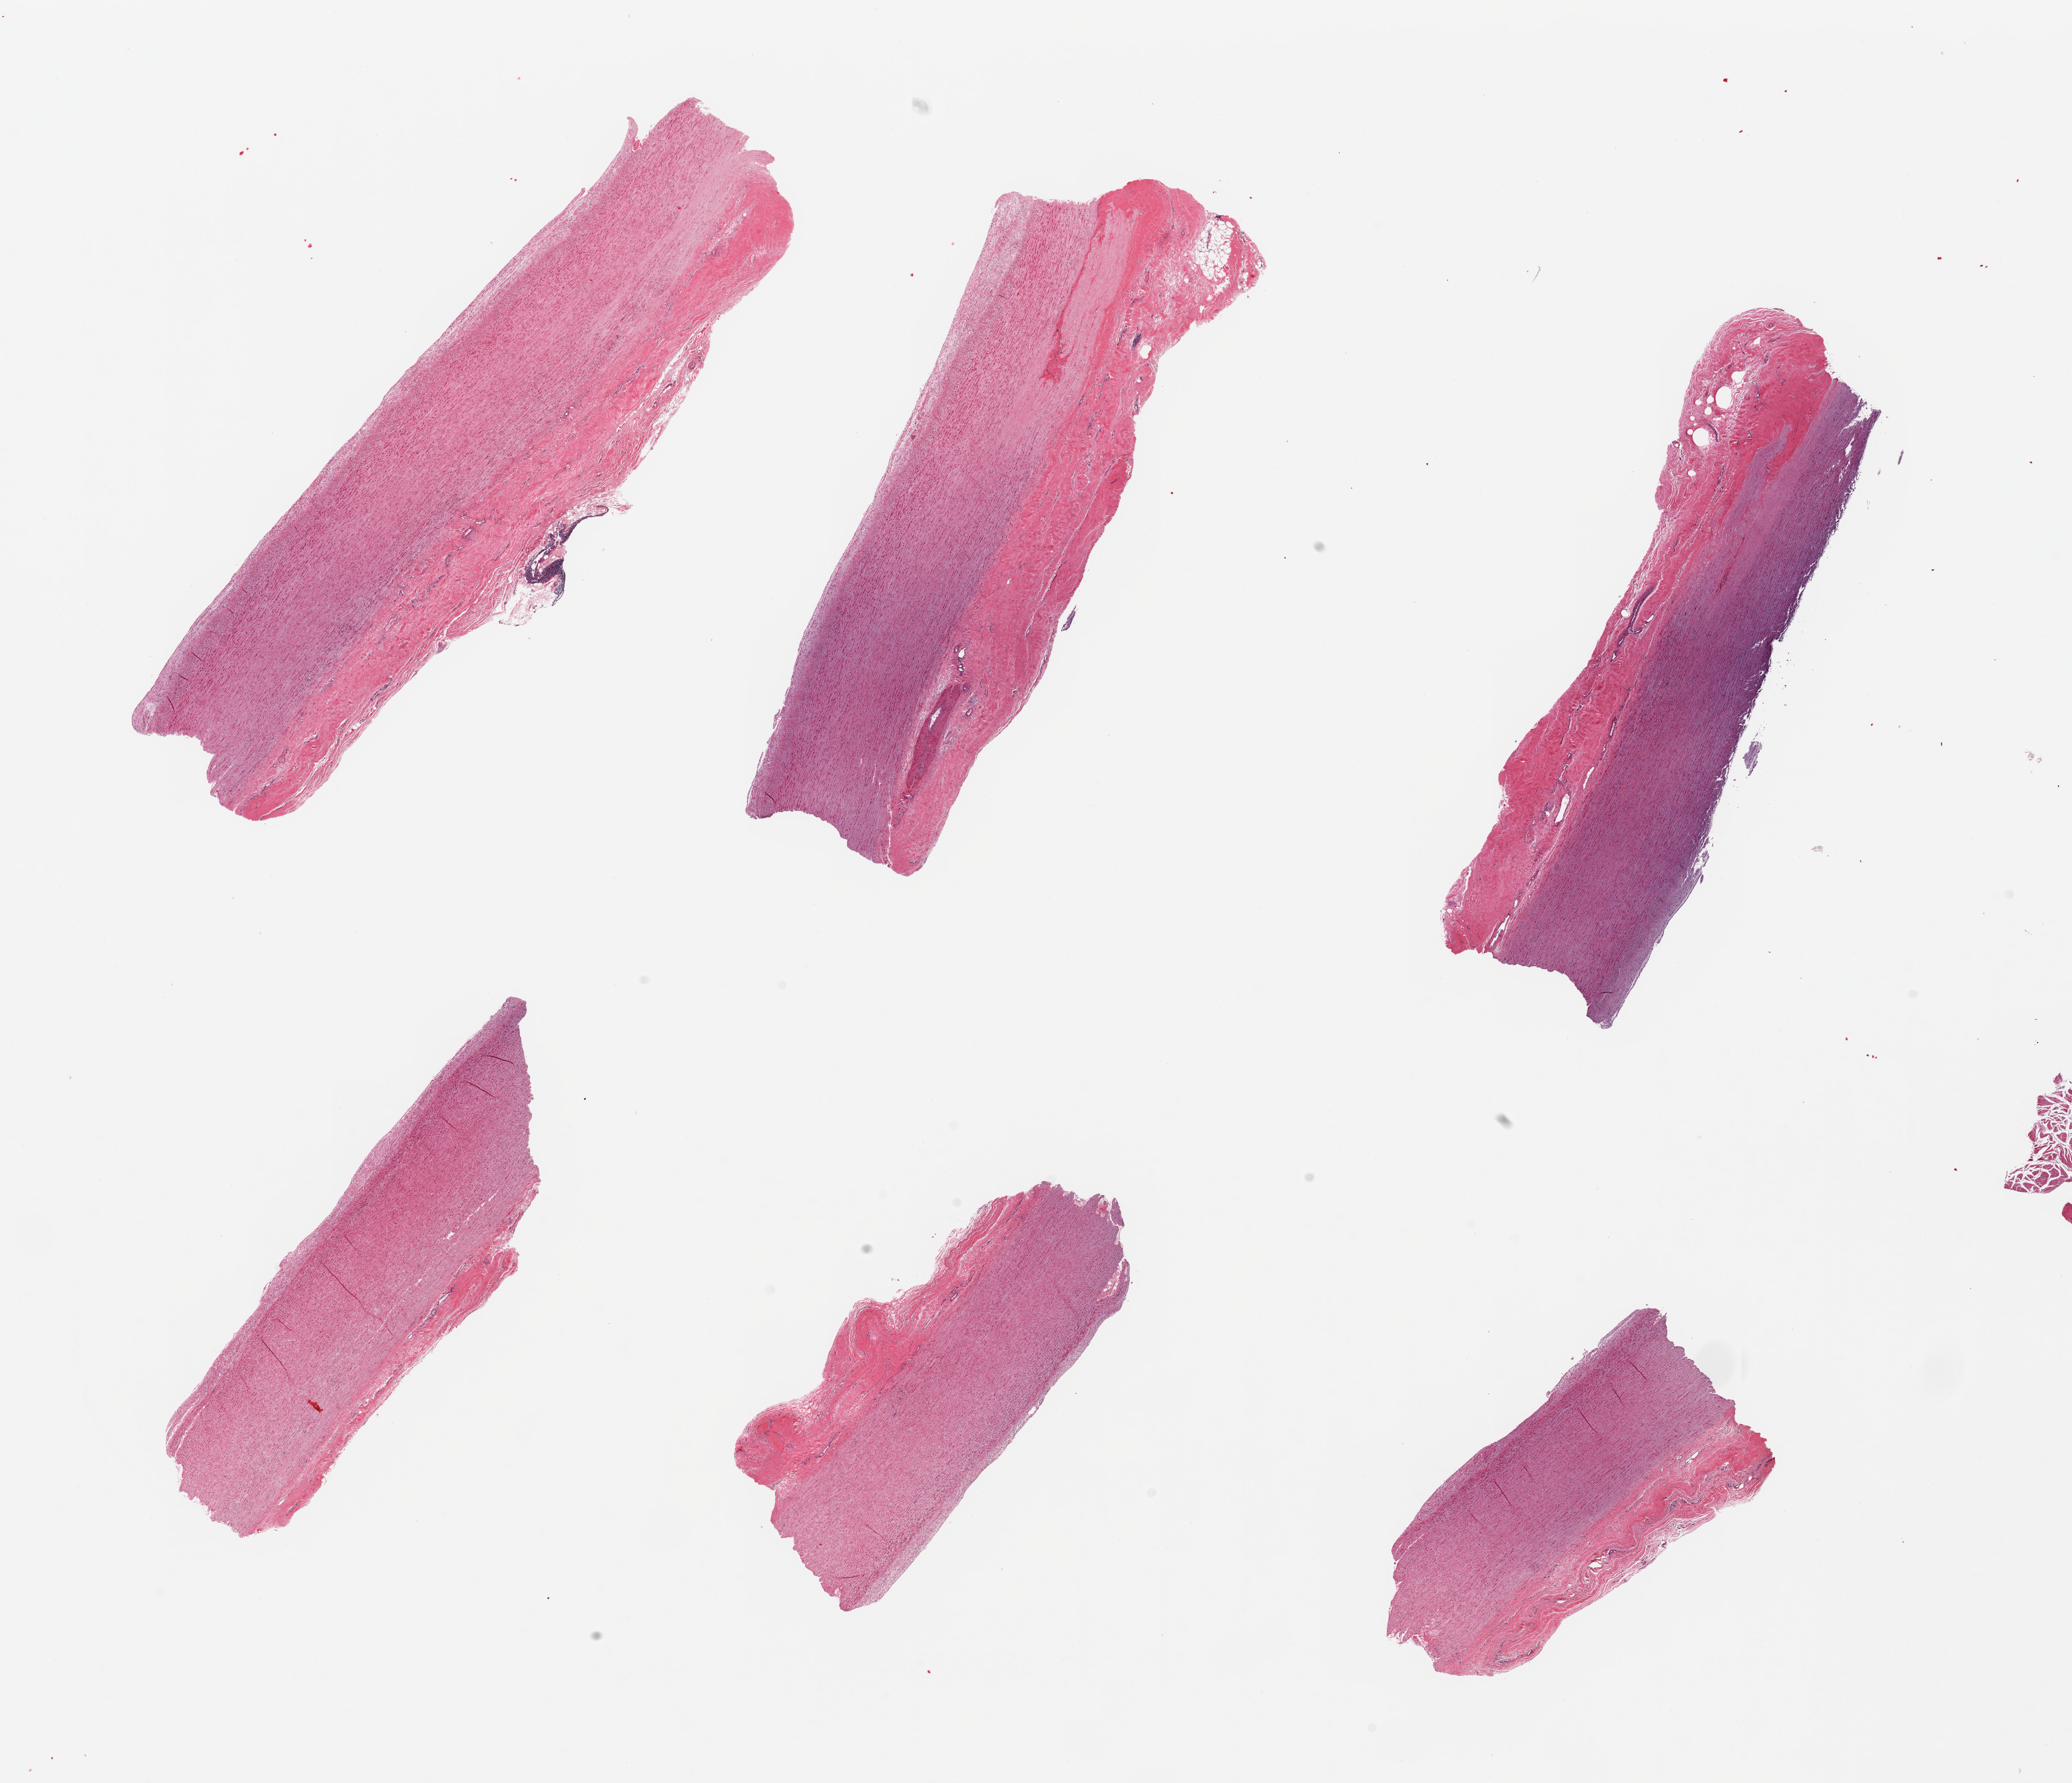
Digitized hematoxylin and eosin (H&E)-stained section, brightfield, whole scanned area (about 24.6 x 21.2 mm, from a 20x scan) shown as a low-resolution overview, PAXgene-fixed, paraffin-embedded tissue, target tissue: aorta, tissue donor sample. Donor: male.
* review note (as recorded): 6 pieces, atherosis up to ~0.2mm